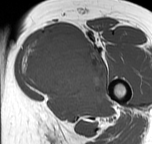
MRI of an extremity soft-tissue mass, one axial slice. Slice 36 of 57 in the series (ordered by position). MR volume resampled by the dataset authors to the PET/CT grid (not the native acquisition matrix). 152 × 144 image matrix. Female patient. Case-level facts recorded for this patient, not image findings: histological type: pleiomorphic leiomyosarcoma; grade: intermediate; site of the primary tumour: left thigh.
Structures marked on this image (expert contour drawn on MRI and transferred to this co-registered scan by the dataset authors):
- gross tumour volume including surrounding oedema: bounding box (x1, y1, x2, y2) in pixels: (18, 33, 105, 102)
- gross tumour volume (mass): (18, 35, 105, 102)